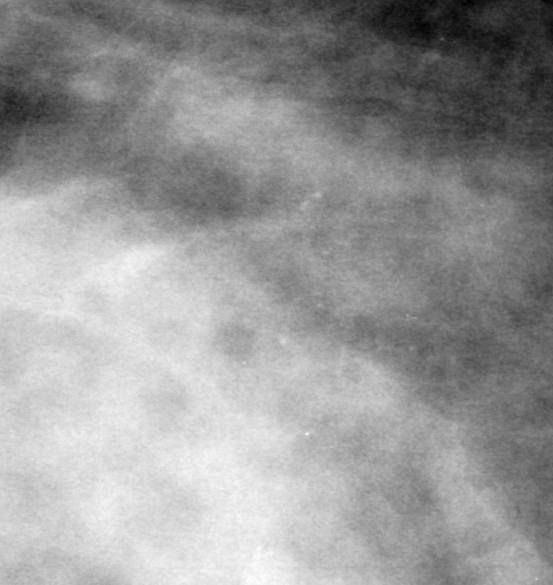
Crop from a digitized film mammogram around one marked abnormality, right breast, CC view.
Finding: calcifications, morphology punctate / amorphous, distribution clustered; BI-RADS assessment category 0 (incomplete: needs additional imaging); pathology (as recorded): benign.